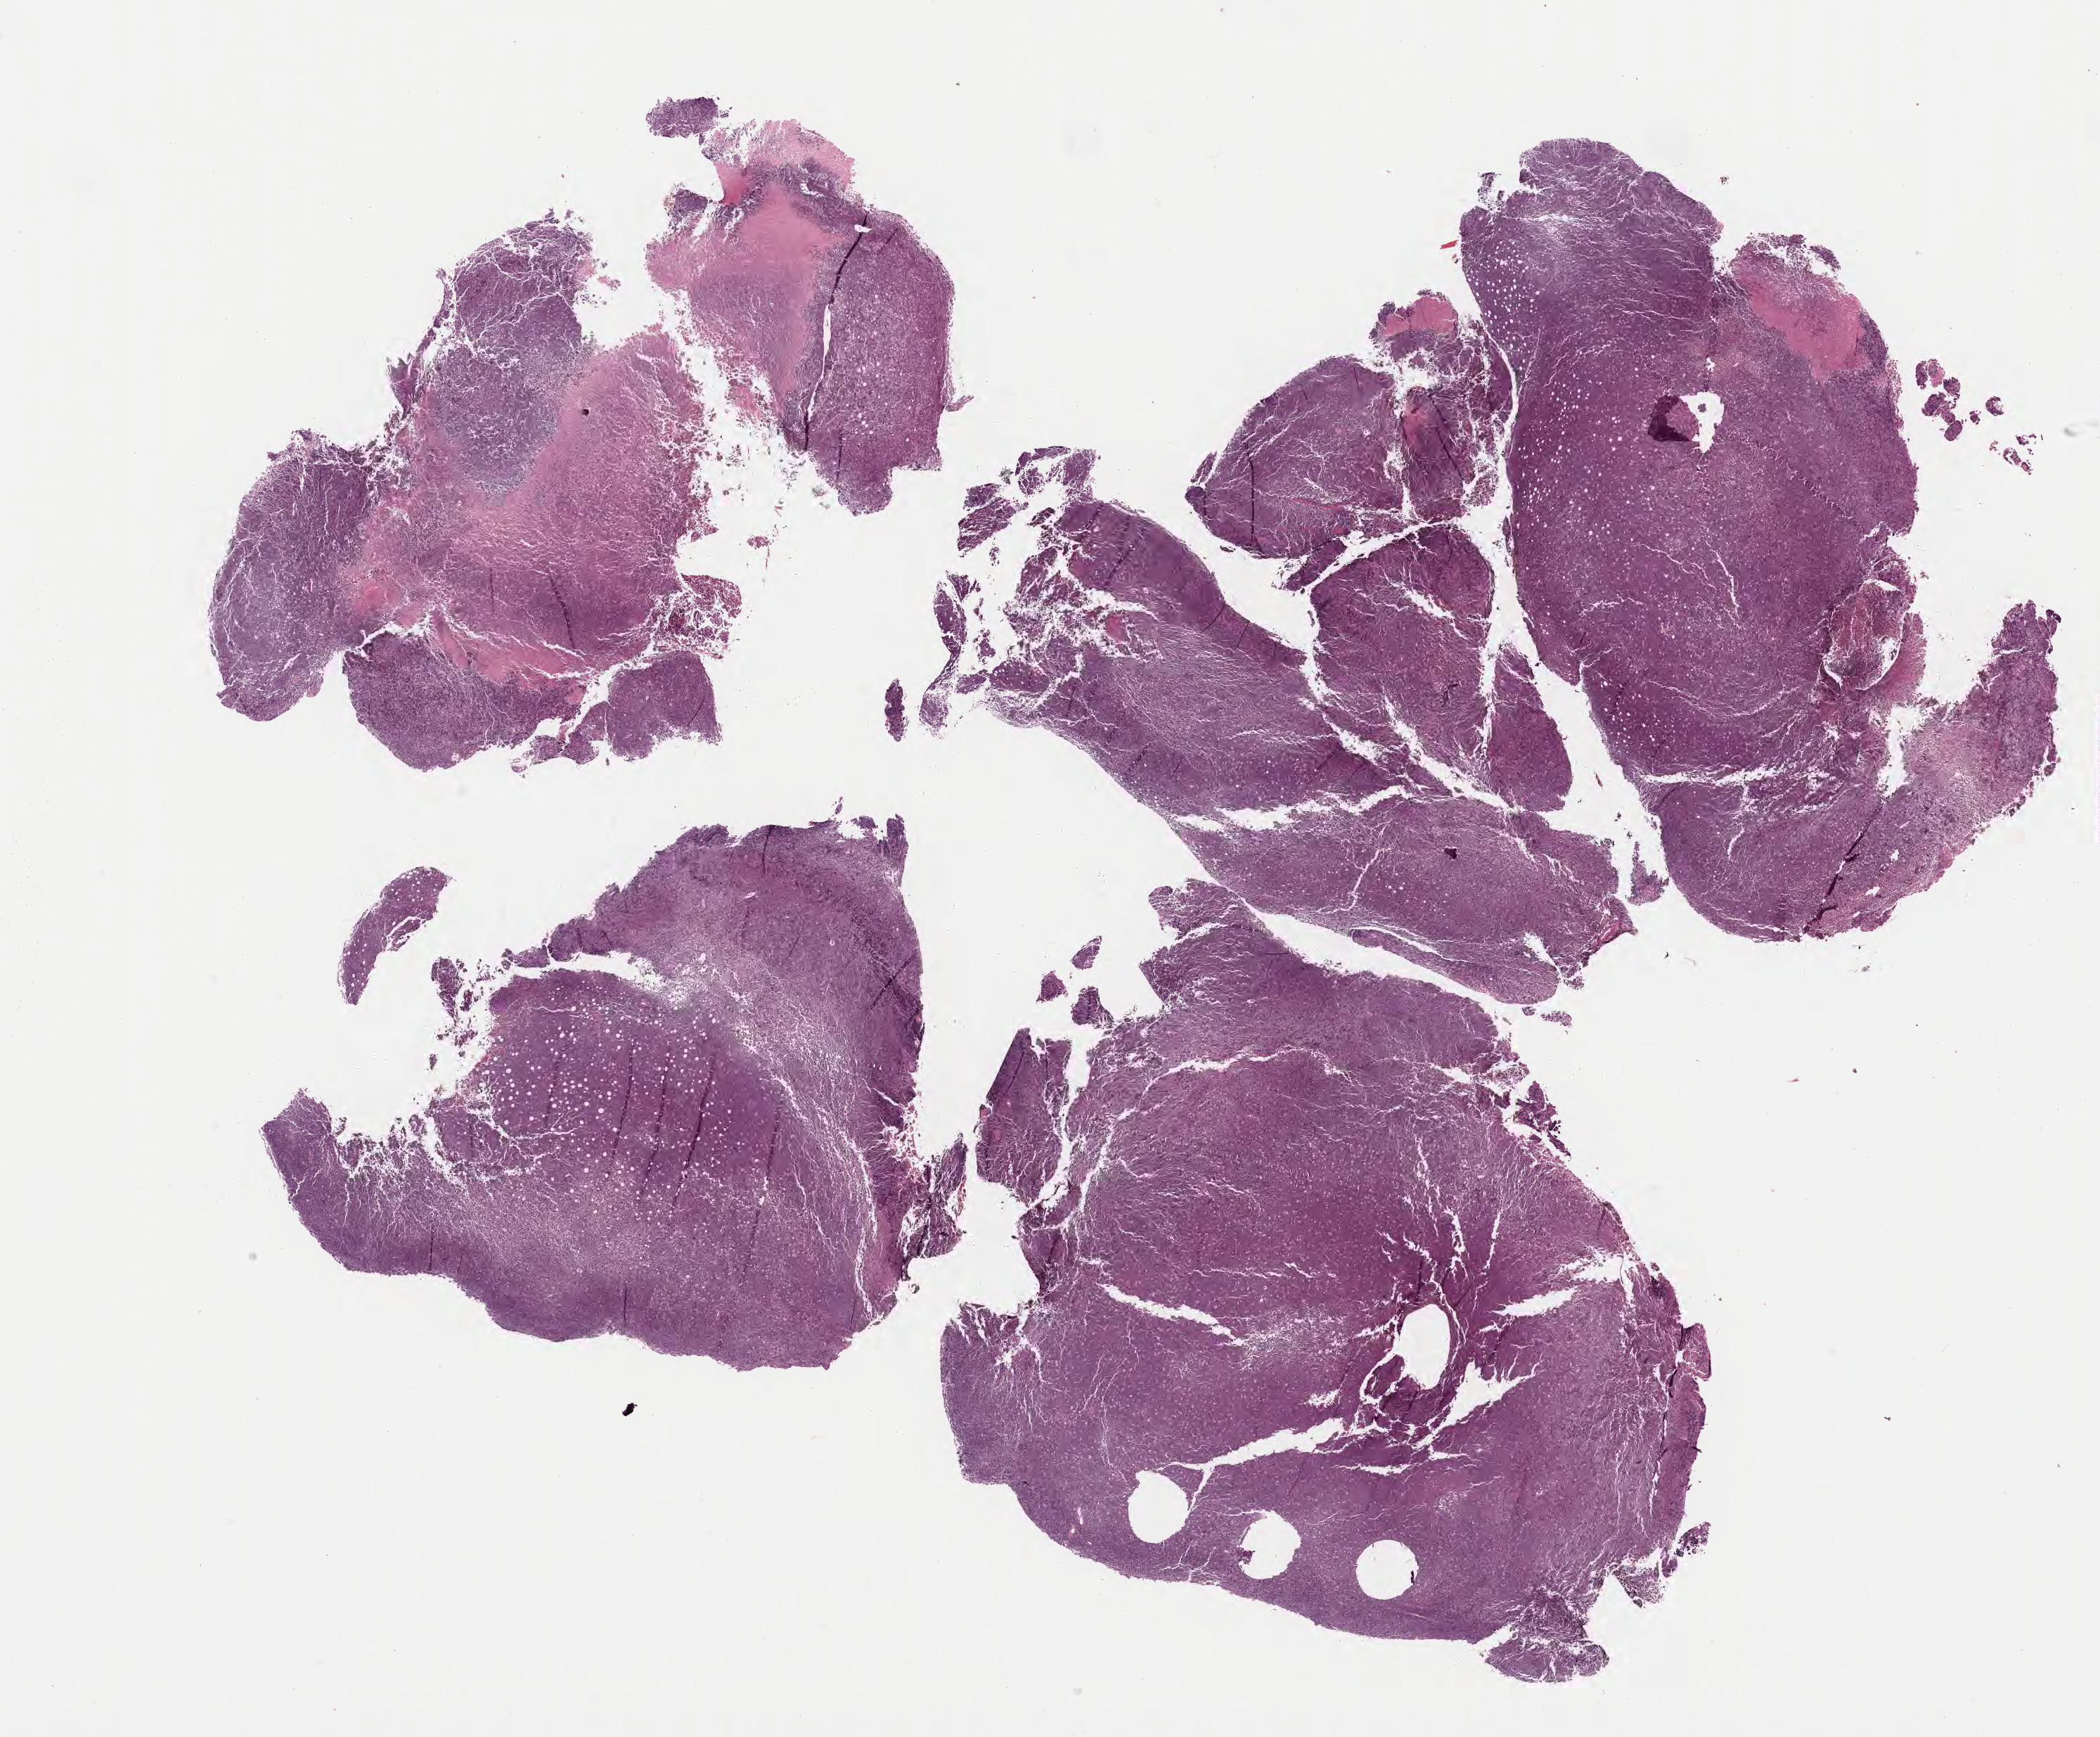
H&E whole-slide image, a low-resolution overview of the entire scanned area, about 24.2 x 20.0 mm. FFPE section. Primary tumor. Patient: male, age 60 years. Composition of this section per pathologist review: tumor cells 75%, tumor nuclei 90%, stromal cells 5%, necrosis 20%, normal cells 0%. Inflammatory infiltration, as recorded: lymphocyte infiltration 50%, monocyte infiltration 25%, neutrophil infiltration 5%.
• diagnosis: Diffuse large B-cell lymphoma, NOS
• Ann Arbor stage (patient): Stage IV